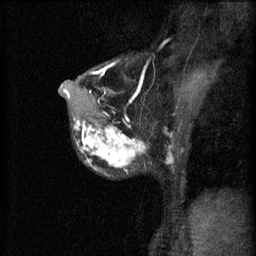
Breast MRI (dynamic contrast-enhanced), one sagittal slice. Position 40 of 60 along the scan axis. 3 images stored at this slice position (order not interpretable as contrast timing). 1.5 T. TE 4.2 ms, TR 11 ms. 2 mm slice thickness. 256 × 256 image matrix. Female patient, age 37 years.
Annotated regions visible in this slice (semi-automatically segmented with operator editing):
- analysis volume of interest (the breast-tissue region the enhancement analysis was run in; not a lesion): box from (x=71, y=118) to (x=176, y=177) px
- tumour enhancement mask (voxels above the 70 % enhancement threshold inside the analysis volume of interest): (x=73, y=118)–(x=173, y=171)